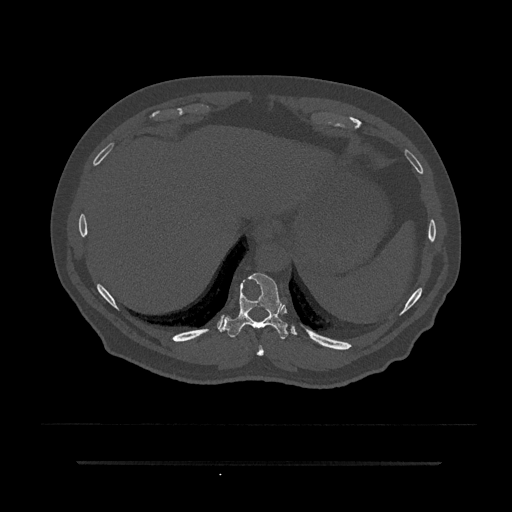
CT including the spine, one axial slice; position 331 of 797 along the scan axis; 120 kVp; bone window (W 1800 / L 400 HU); 0.5 mm slice thickness; 512 × 512 image matrix. Male patient, age 59 years. Case-level facts recorded for this patient, not image findings: primary cancer: bile ducts.
Structures marked on this image (semi-automatically segmented with operator editing):
- T10 vertebra: bounding box (x1, y1, x2, y2) in pixels: (221, 273, 297, 339)
- T9 vertebra: (256, 345, 264, 356)